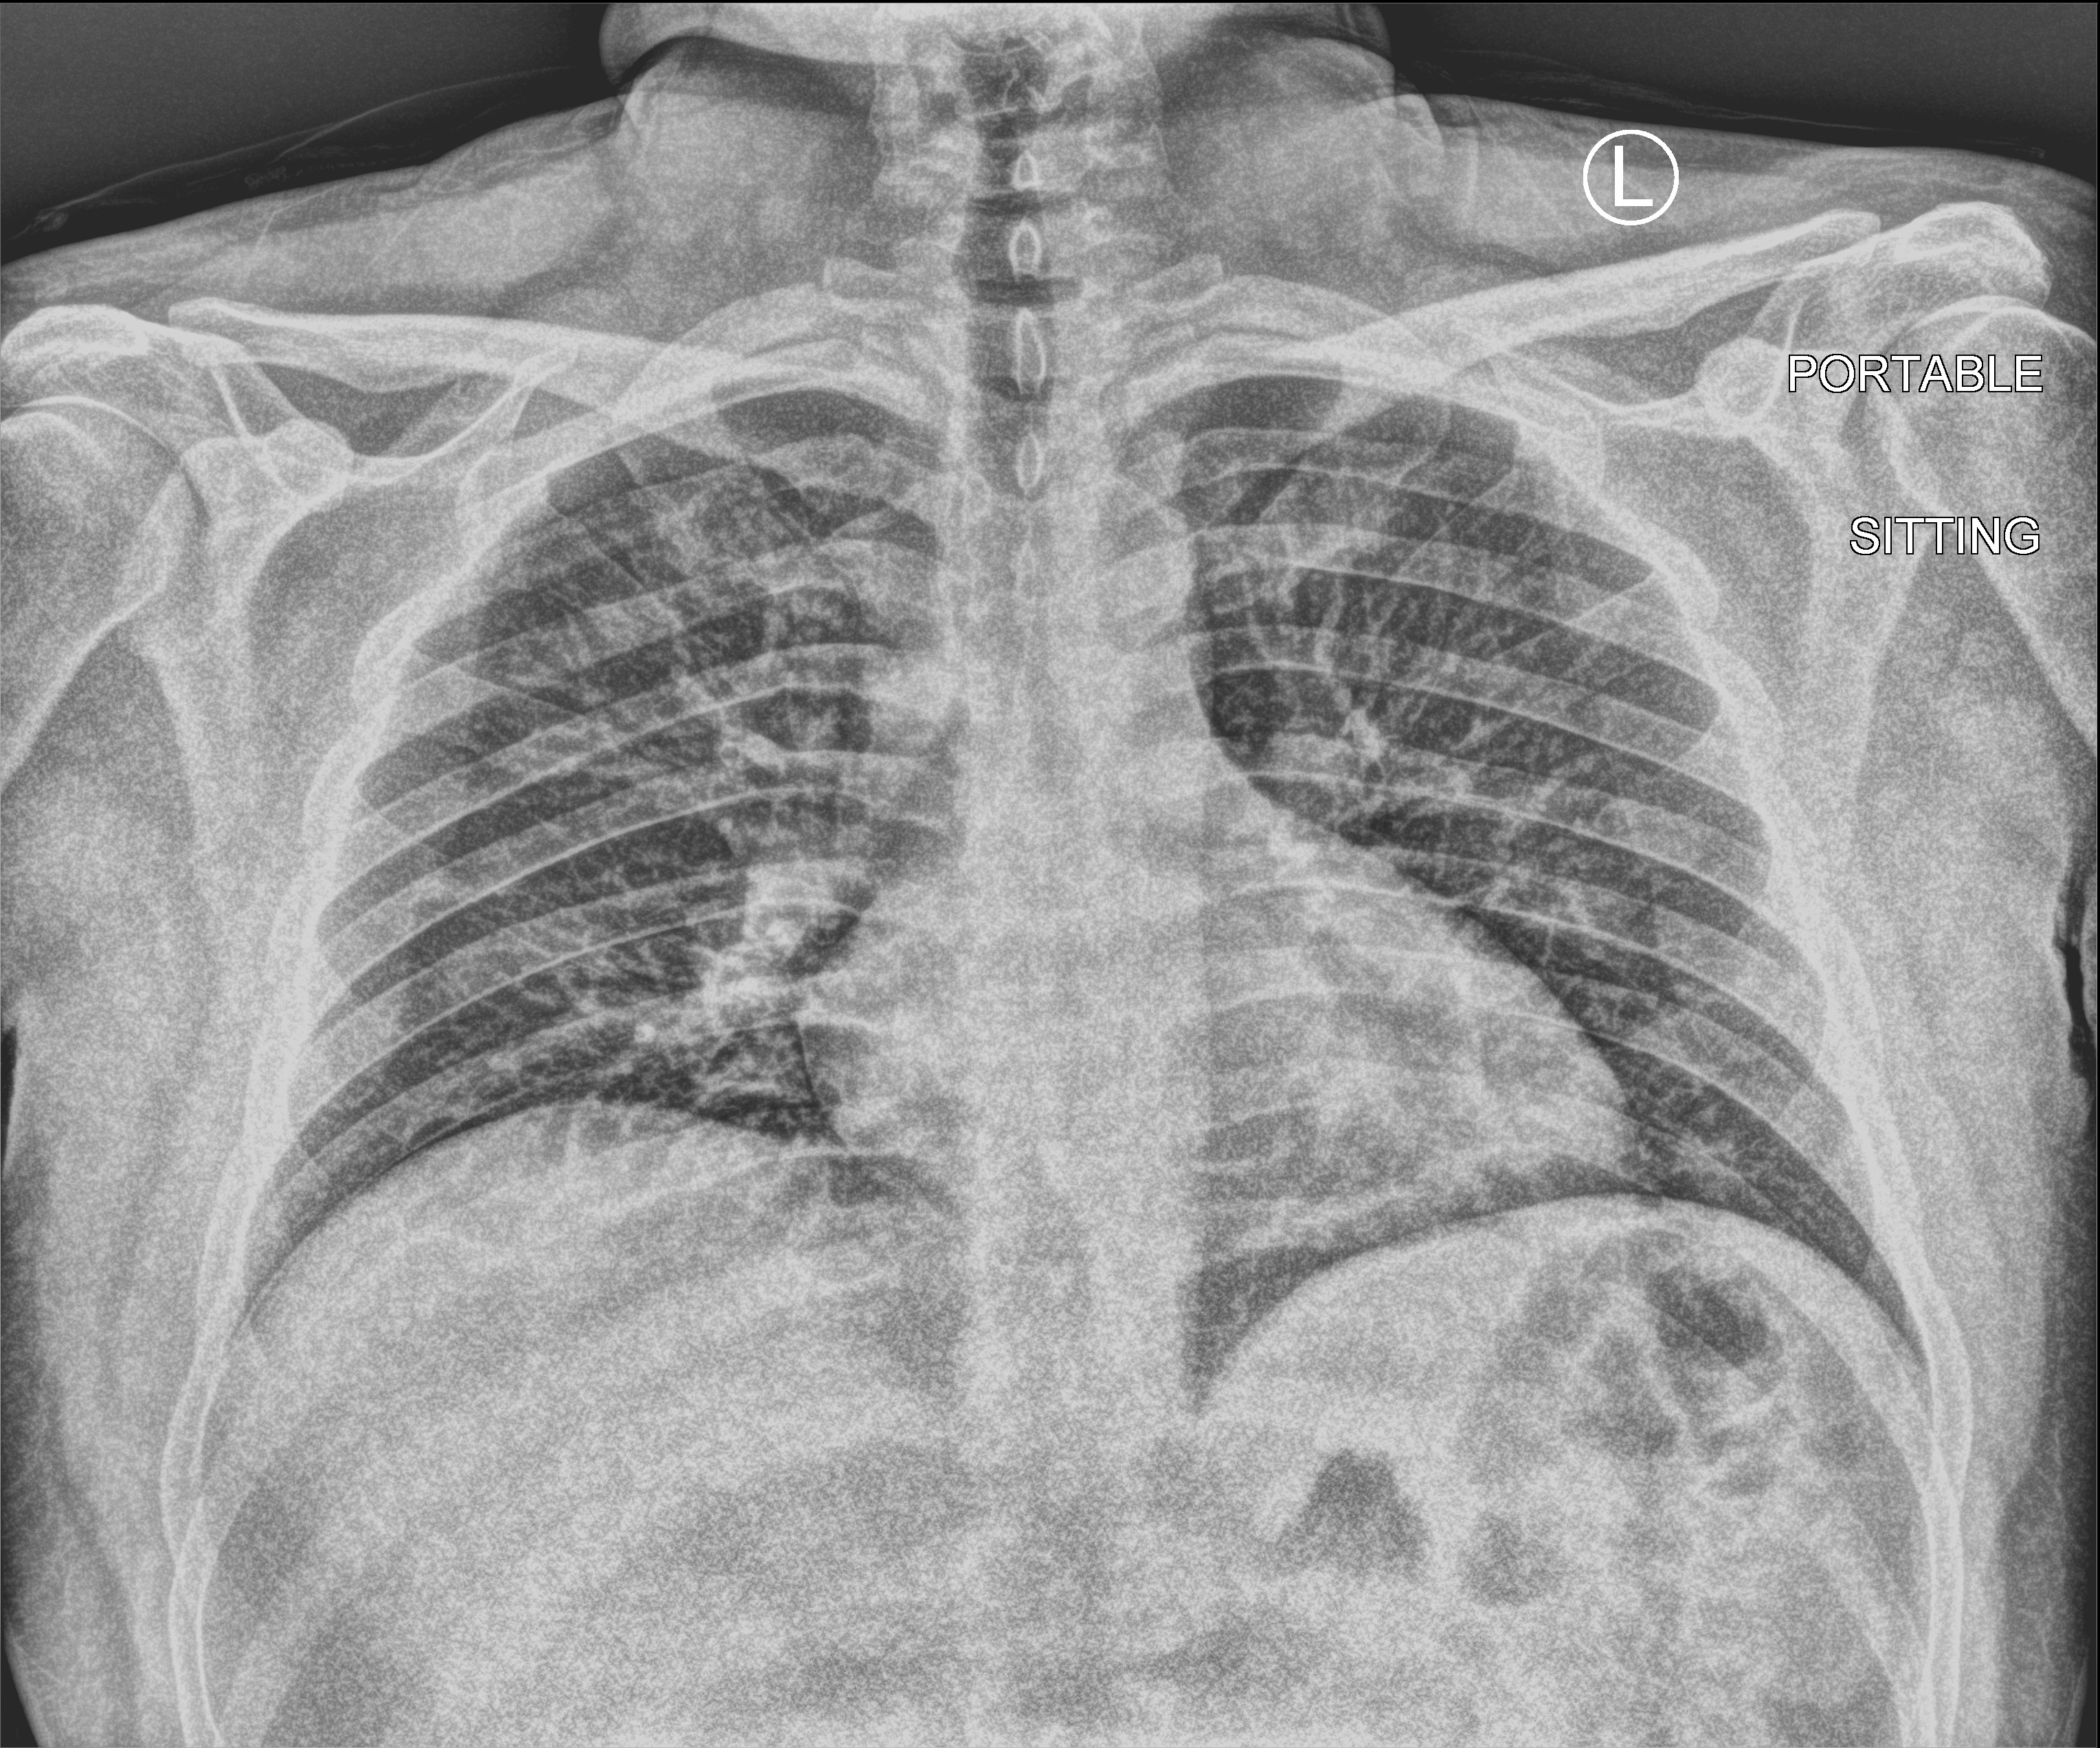
Bedside chest radiograph (computed radiography), anteroposterior (AP) projection. Male patient hospitalised with COVID-19, age 18–59 years.
Admission-level facts for this patient (not findings on this image; timing relative to this image not recorded):
- mechanically ventilated during this hospital stay: no